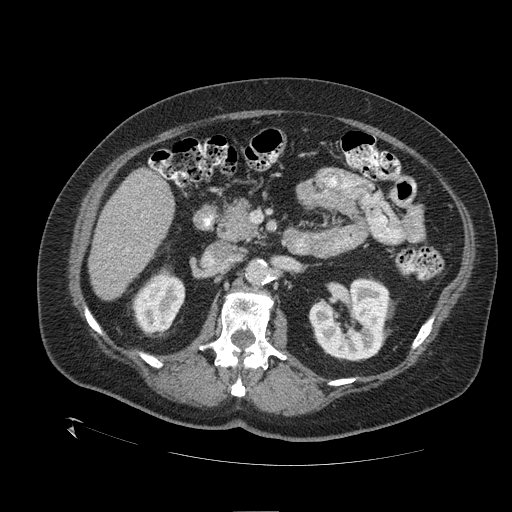
Contrast-enhanced abdominal CT (liver protocol), one axial slice; slice 51 of 109 in the series (ordered by position); reconstruction kernel STANDARD; 120 kVp; one of 2 acquisitions stored at this slice position; soft-tissue window (W 400 / L 40 HU); 2.5 mm slice thickness; 512 × 512 image matrix. Case-level facts recorded for this patient, not image findings: diagnosis: hepatocellular carcinoma (patient treated with transarterial chemoembolisation; whether this scan precedes or follows treatment is not stated here); TNM stage (as recorded): Stage-I; Child-Pugh class: A; tumour differentiation: no biopsy; tumour size: 4.6 cm.
Annotated regions visible in this slice (semi-automatic segmentation, software-assisted and operator-edited):
- liver parenchyma outside the tumour (the mass and vessels are separate outlines, so this box may not span the whole liver): bounding box [x1, y1, x2, y2] px = [88, 168, 174, 300]